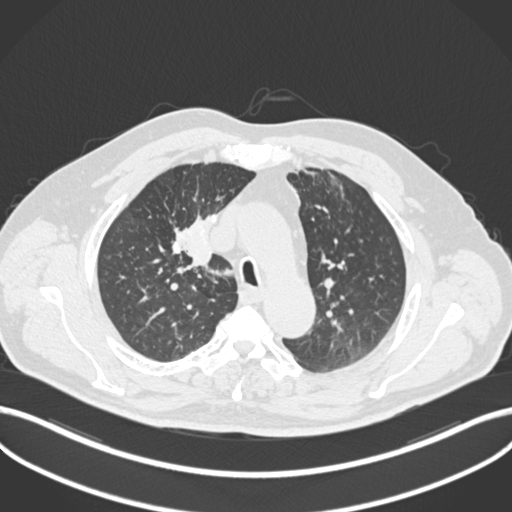
Chest CT, one axial slice; slice 145 of 255 in the series (ordered by position); lung window (W 1500 / L -600 HU); 1 mm slice thickness; 512 × 512 image matrix. Patient: male, 60 years. Case-level facts recorded for this patient, not image findings: clinical TNM (as recorded): T1b N1 M0.
Annotated regions visible in this slice (bounding box drawn by a radiologist):
- lung tumour (recorded histology: squamous cell carcinoma): box from (x=171, y=216) to (x=217, y=281) px